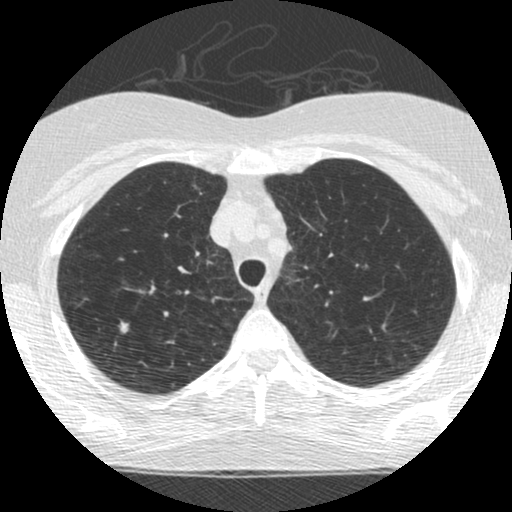
Low-dose screening chest CT, one axial slice. Position 206 of 253 along the scan axis. Reconstruction kernel STANDARD. Lung window (W 1500 / L -600 HU). 1.25 mm slice thickness. 512 × 512 image matrix, field of view 294 × 294 mm.
Structures marked on this image (manually delineated by an expert):
- lesion 1 (tumor, upper lobe of right lung): bounding box [x1, y1, x2, y2] px = [119, 319, 130, 333]